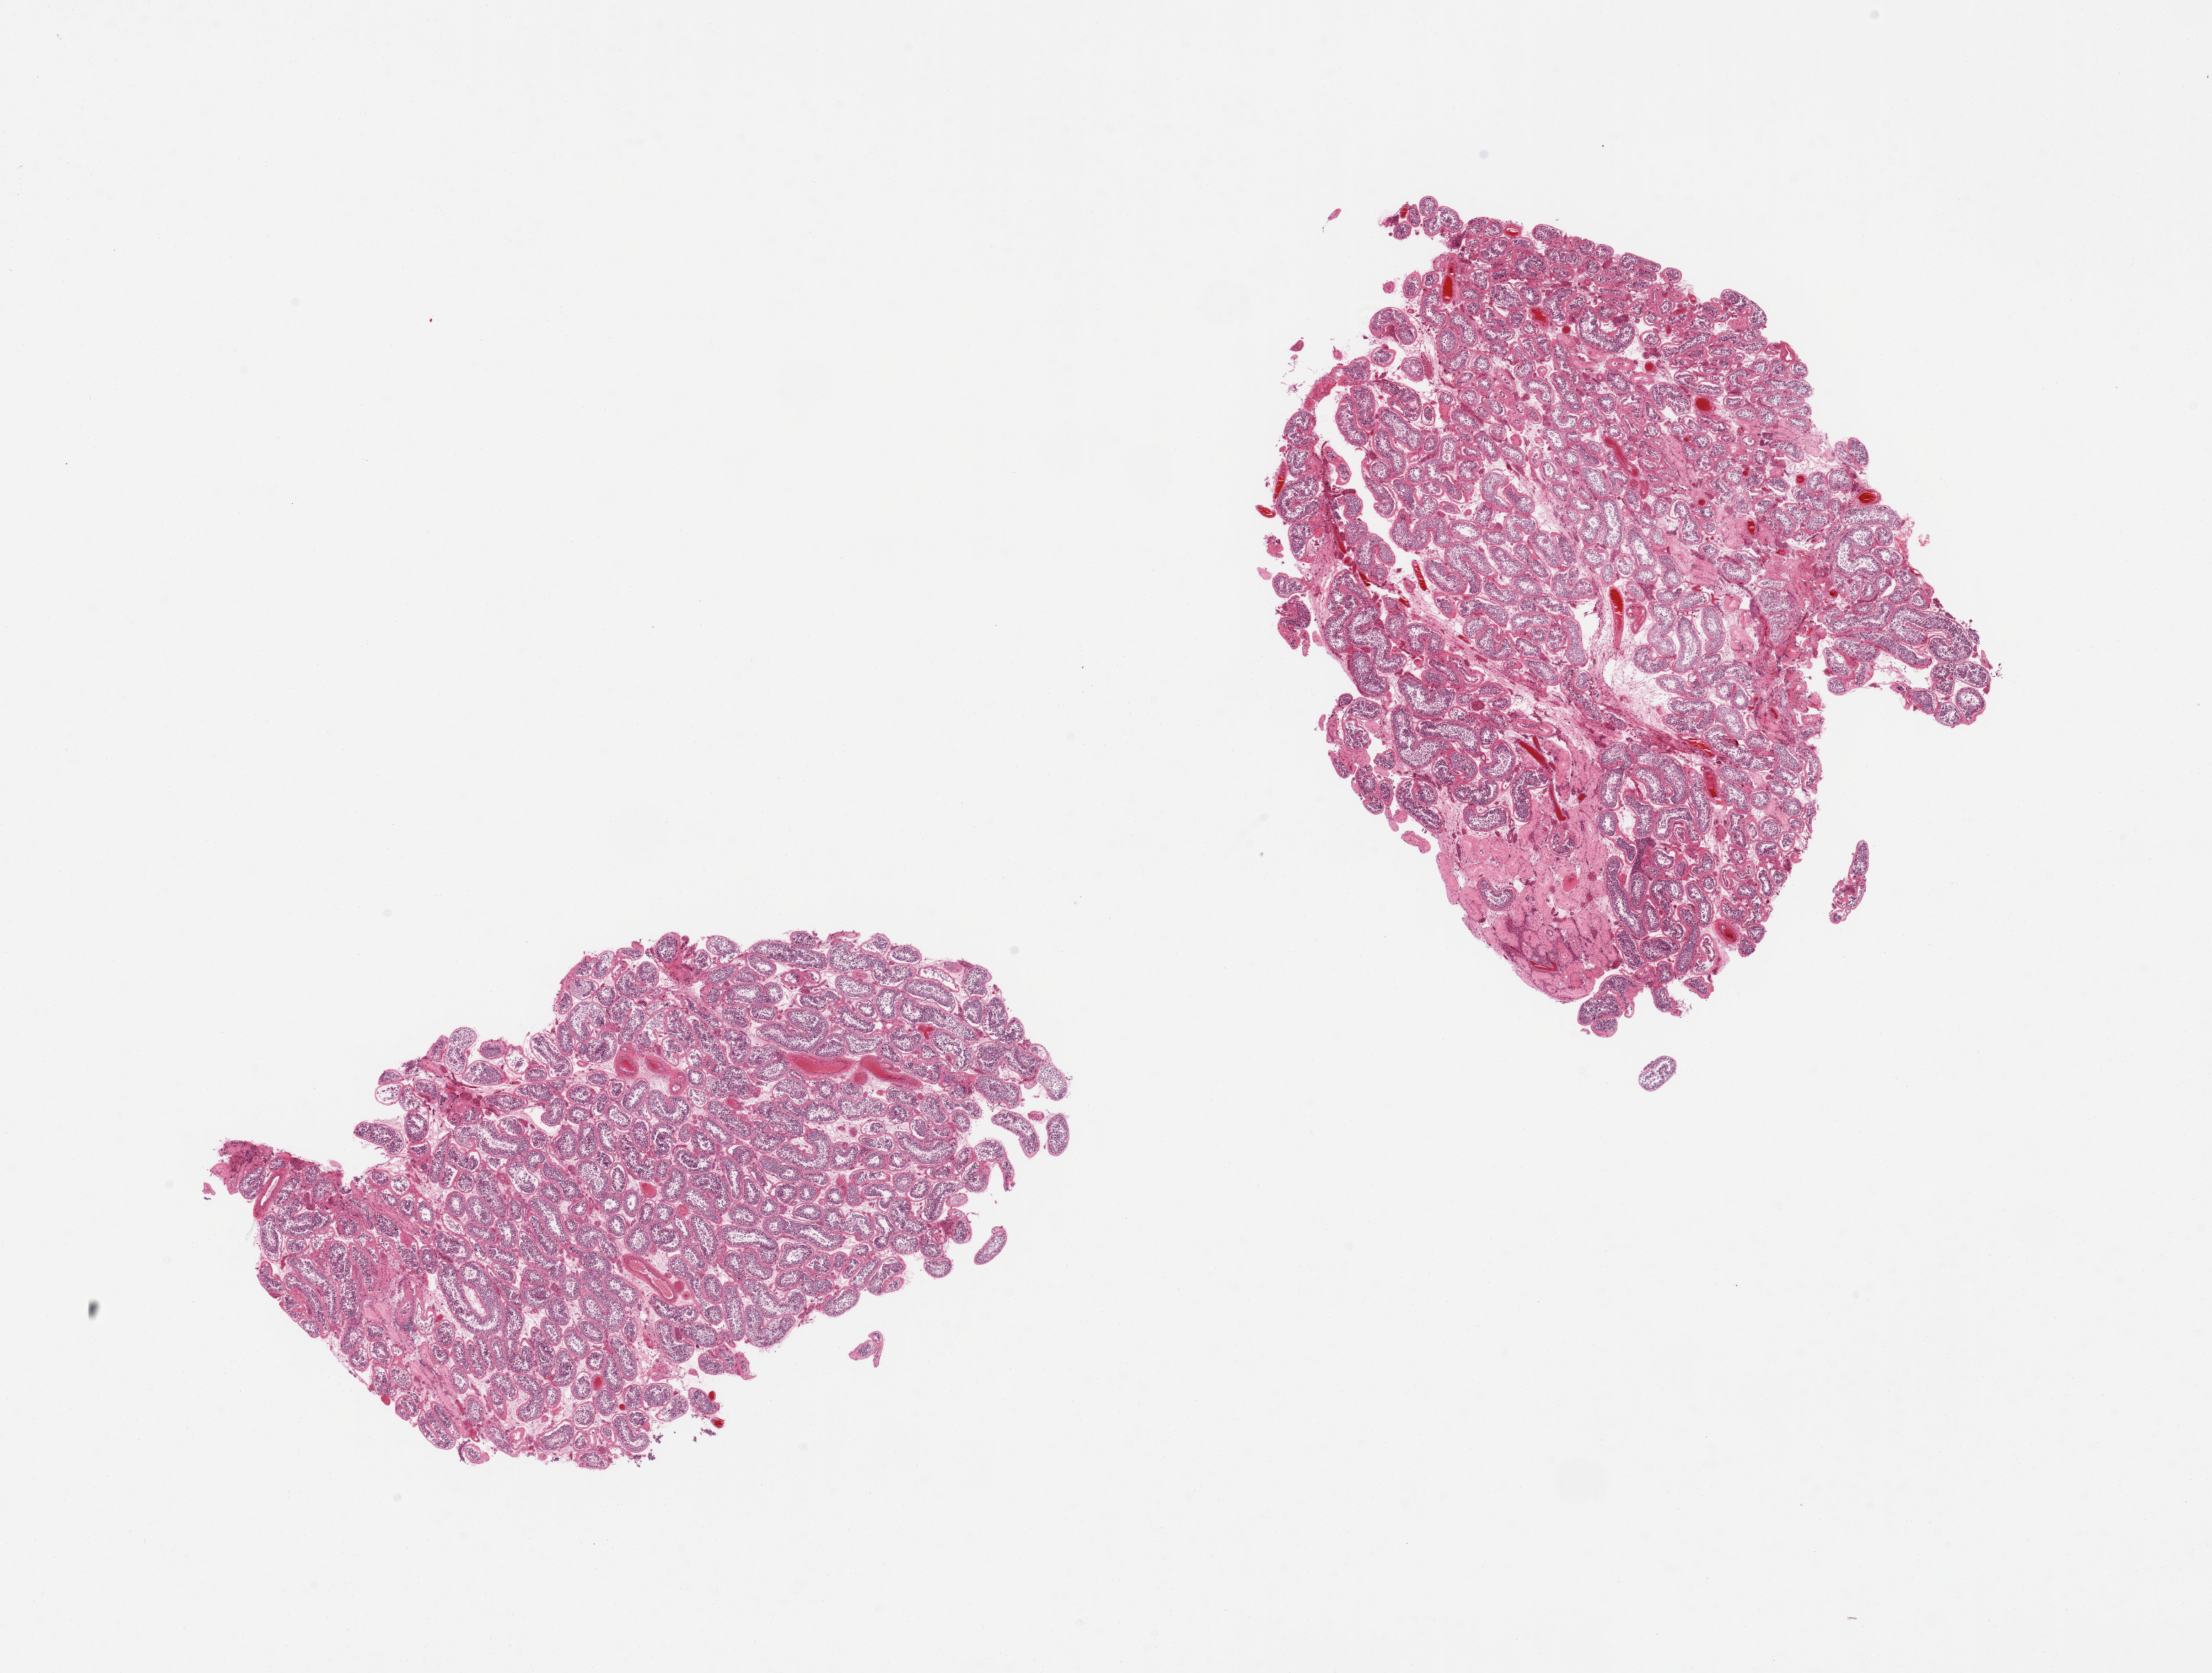
Whole-slide image, haematoxylin and eosin stain, shown as a low-resolution overview of the whole scanned area (about 24.6 x 18.6 mm), PAXgene-fixed, paraffin-embedded tissue, sampled site (target tissue): testis, tissue donor sample.
Reviewer comment on this tissue sample: 2 pieces, spermatogenesis is present, peritubular fibrosis and some hyalinization of tubules.